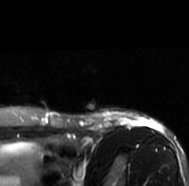
MRI of an extremity soft-tissue mass, one axial slice. Slice 61 of 77 in the series (ordered by position). T2-weighted fat-saturated. MR volume resampled by the dataset authors to the PET/CT grid (not the native acquisition matrix). 3.27 mm slice thickness. 189 × 186 image matrix, field of view 185 × 182 mm. Female patient. From the clinical record (not read from this slice): histological type: leiomyosarcoma; grade: high; site of the primary tumour: groin.
Annotated regions visible in this slice (expert contour drawn on MRI and transferred to this co-registered scan by the dataset authors):
- gross tumour volume including surrounding oedema: bounding box <86,109,160,133> (left, top, right, bottom; pixels)
- gross tumour volume (mass): <95,122,109,128>